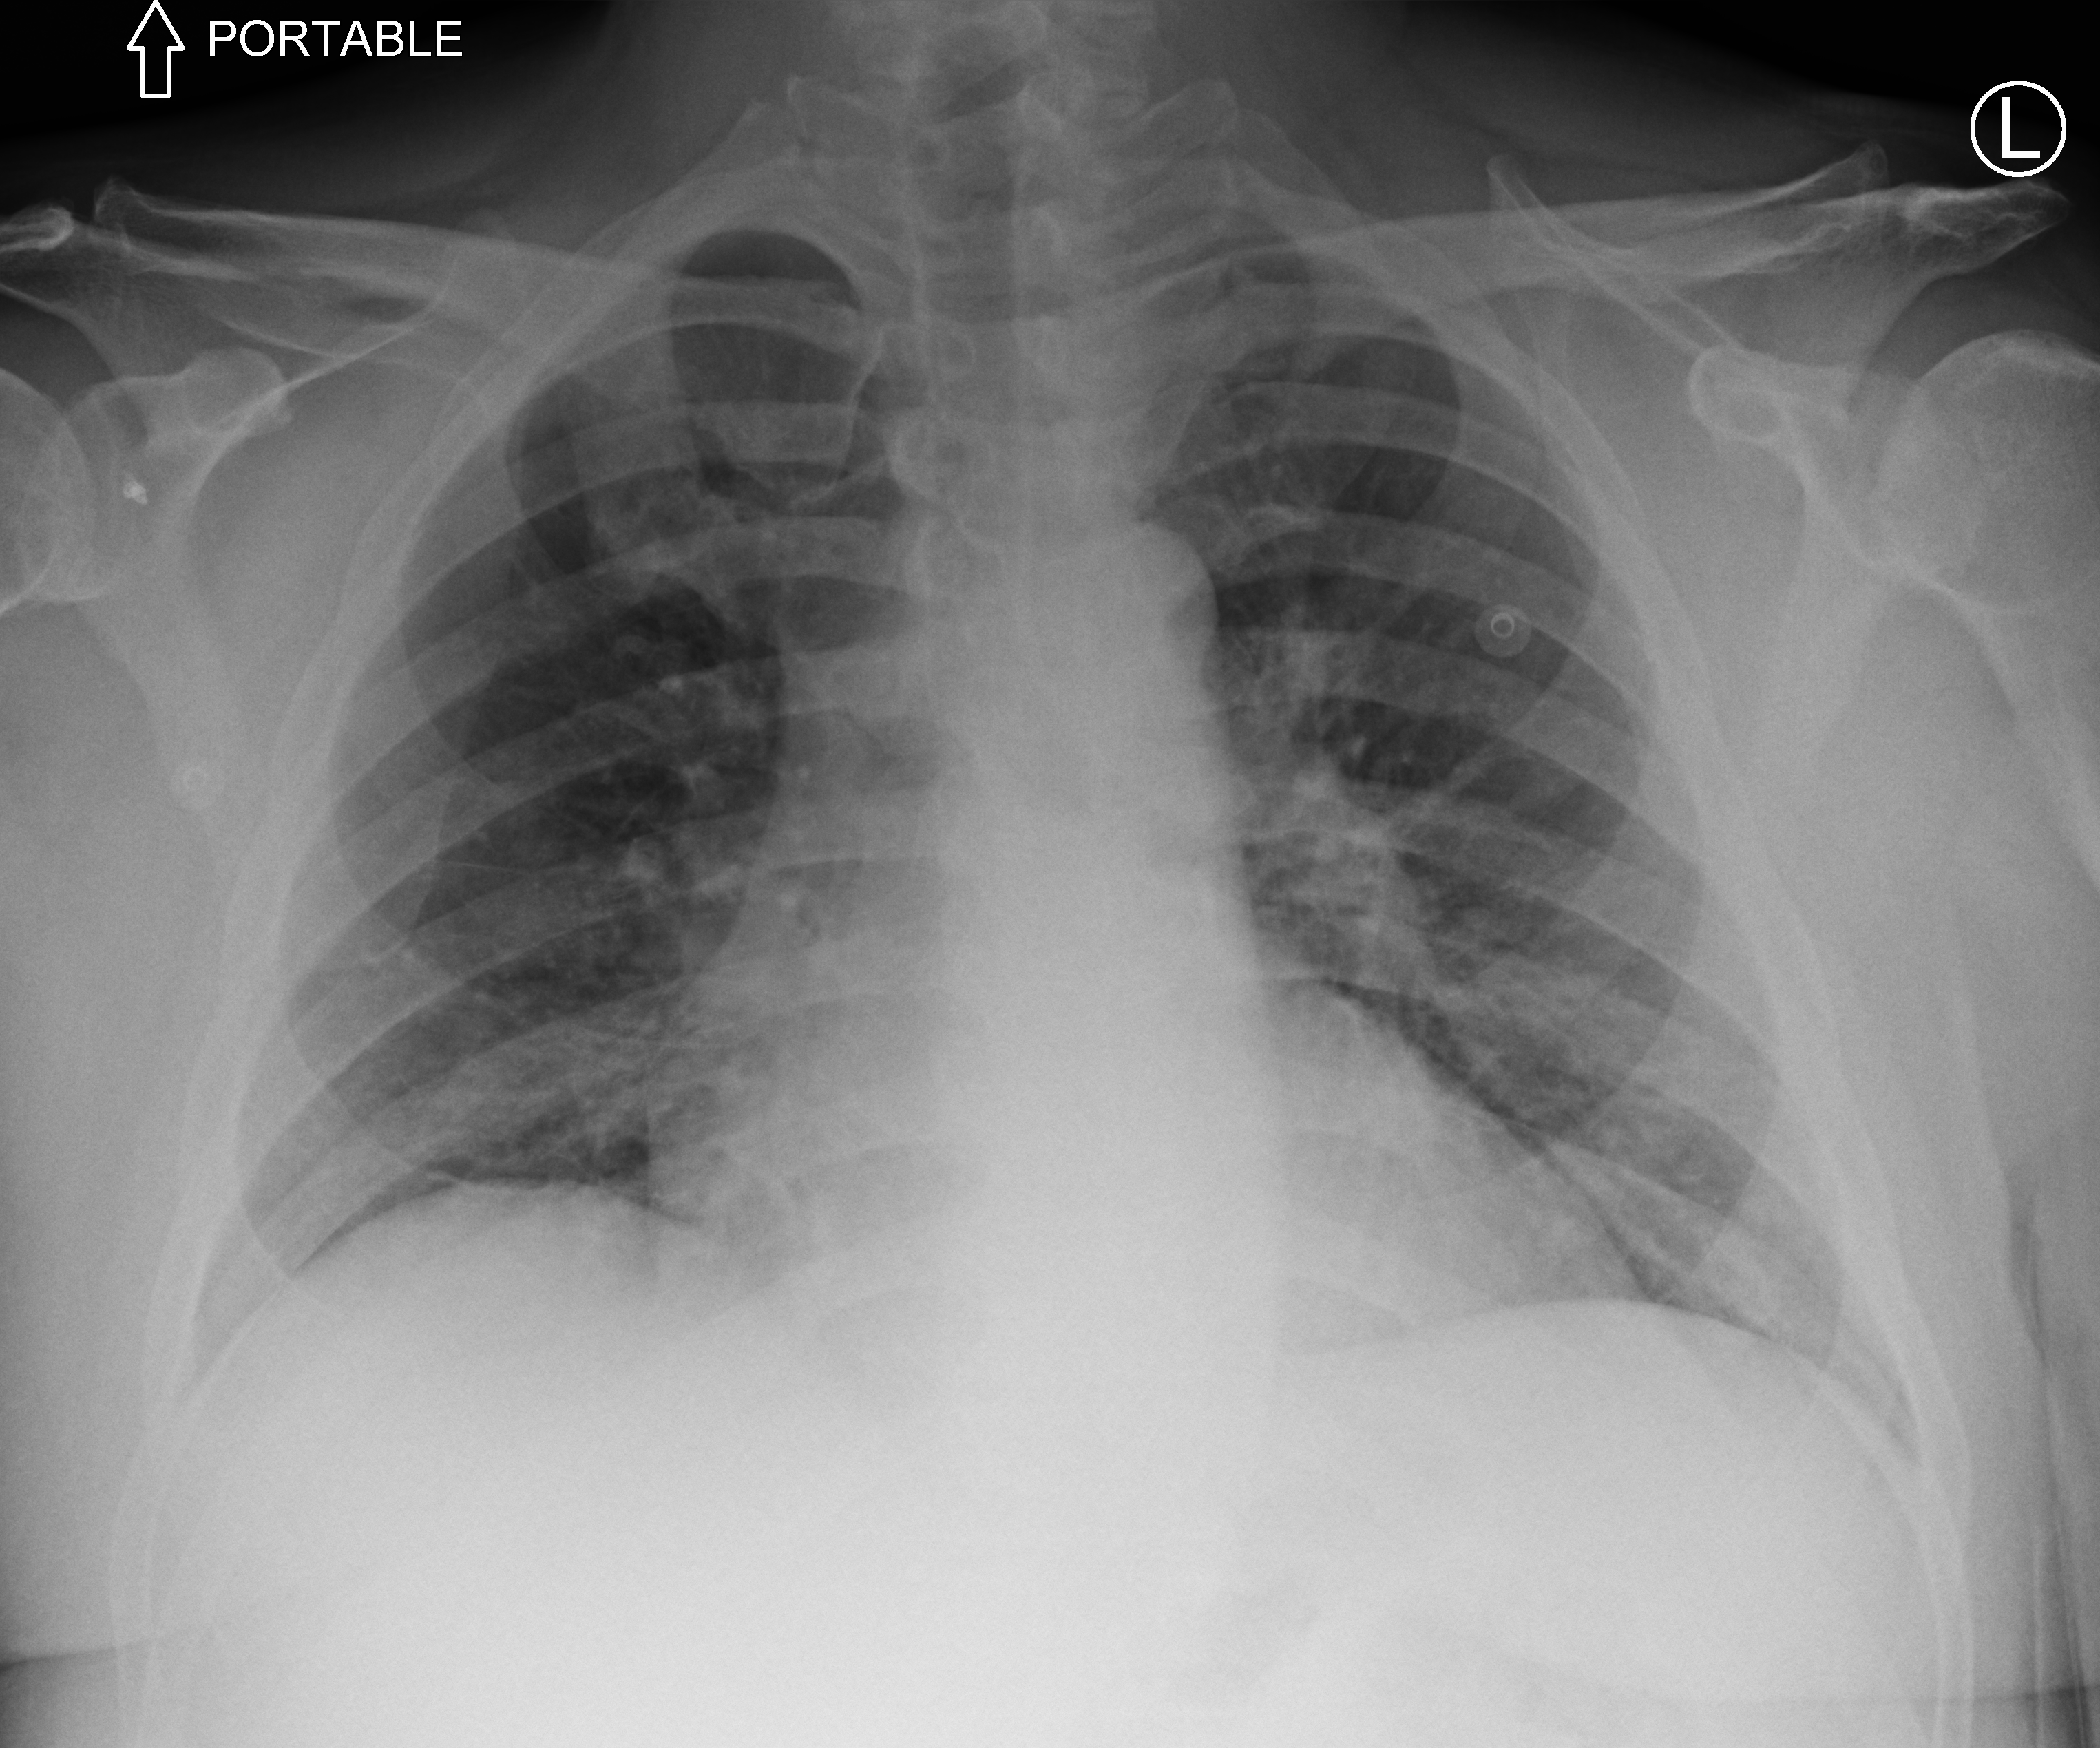
Bedside chest radiograph (computed radiography), anteroposterior (AP) projection. Male patient hospitalised with COVID-19, age 18–59 years.
From the hospital-stay record, not from the radiograph (when in the stay this image was taken is not recorded): smoking status (admission record): never.